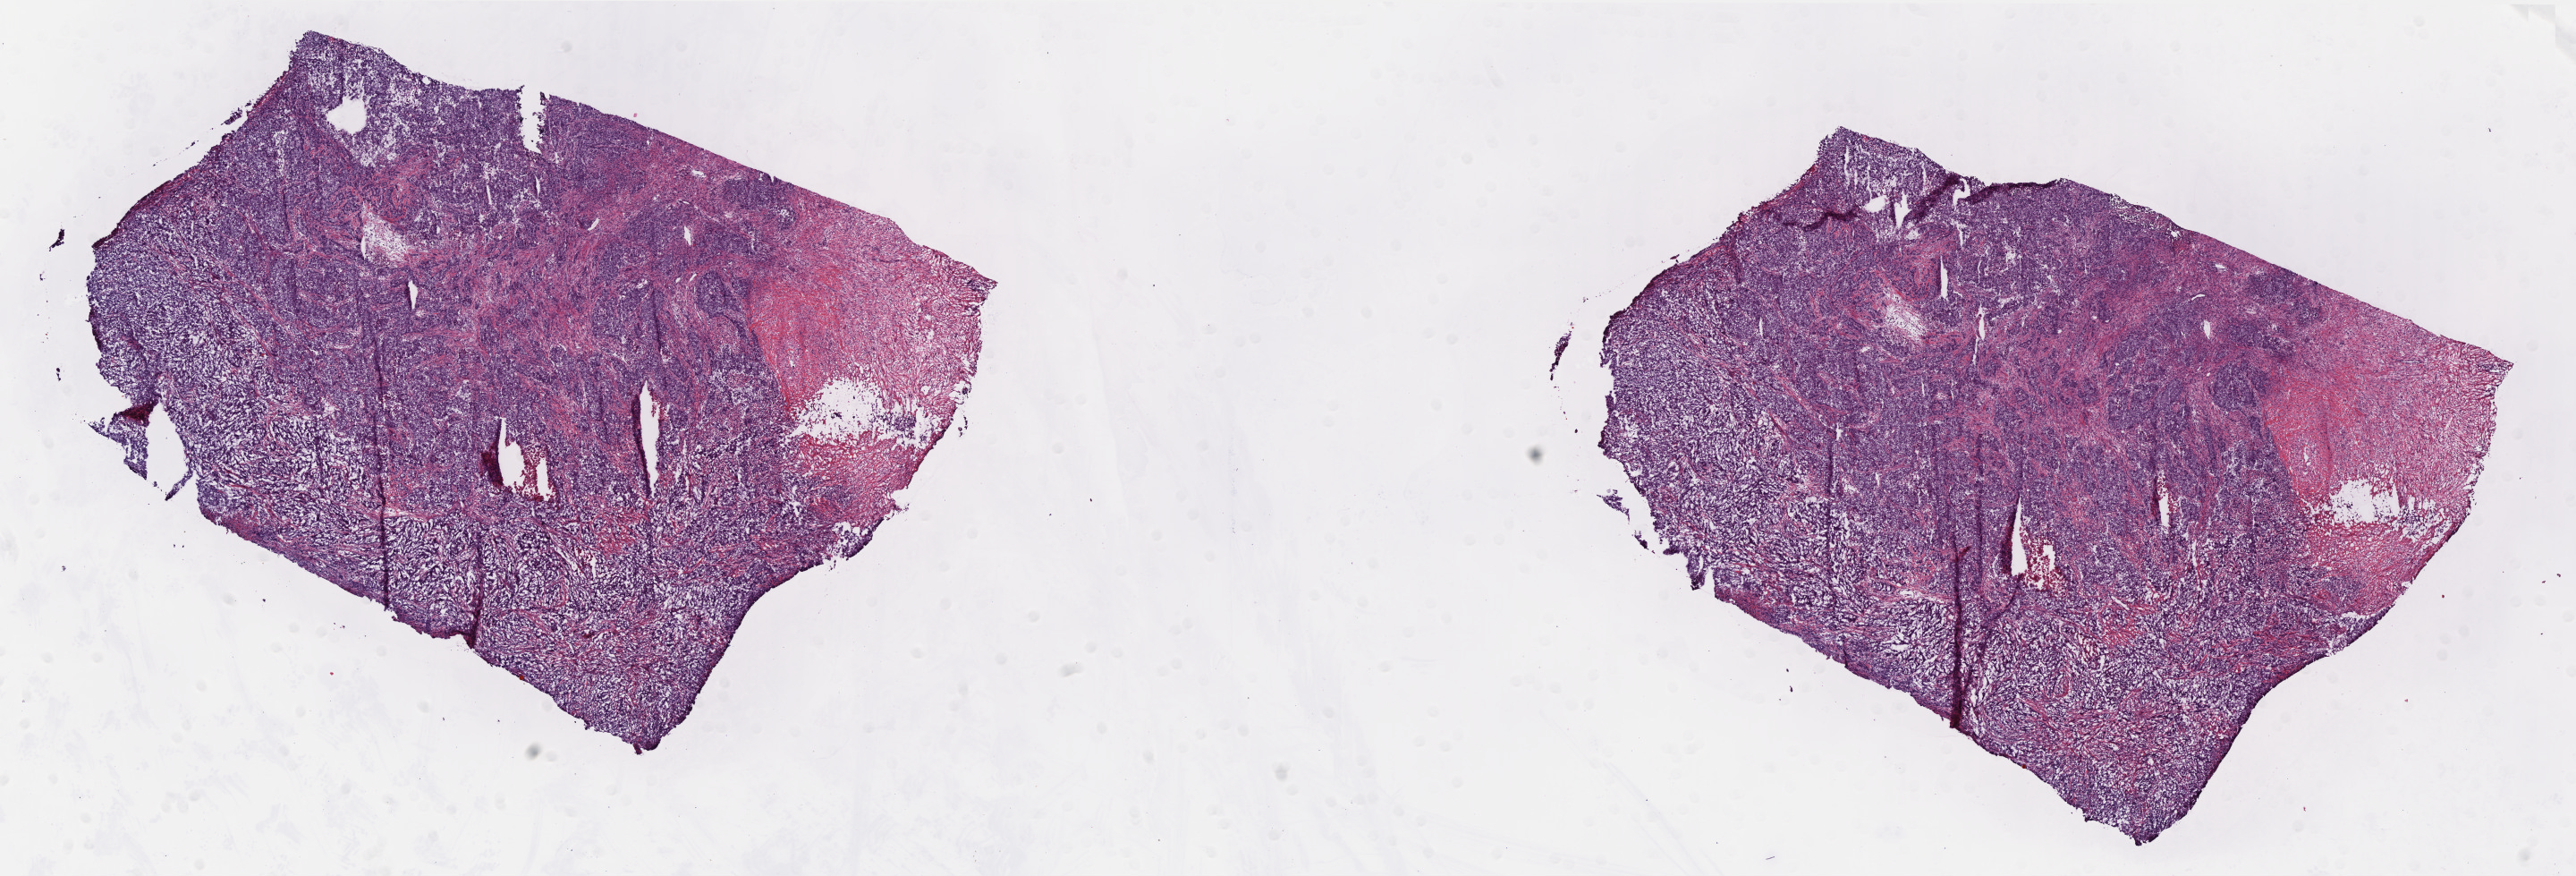
Digitized H&E-stained tissue section (whole slide), whole scanned area (about 23.1 x 7.8 mm) shown as a low-resolution overview; frozen section from the top of the tissue portion; primary tumour sample from the breast. Female, age 56 years at initial diagnosis. Composition of this section per pathologist review: tumour cells 70%, tumour nuclei 80%, normal cells 0%, stromal cells 20%, necrosis 10%. Inflammatory infiltration, as recorded: lymphocyte infiltration 10%, monocyte infiltration 30%, neutrophil infiltration 5%.
Lymph nodes positive (case pathology): 0 of 20 examined. Pathologic diagnosis: Infiltrating duct carcinoma, NOS. AJCC pathologic stage: IIA.